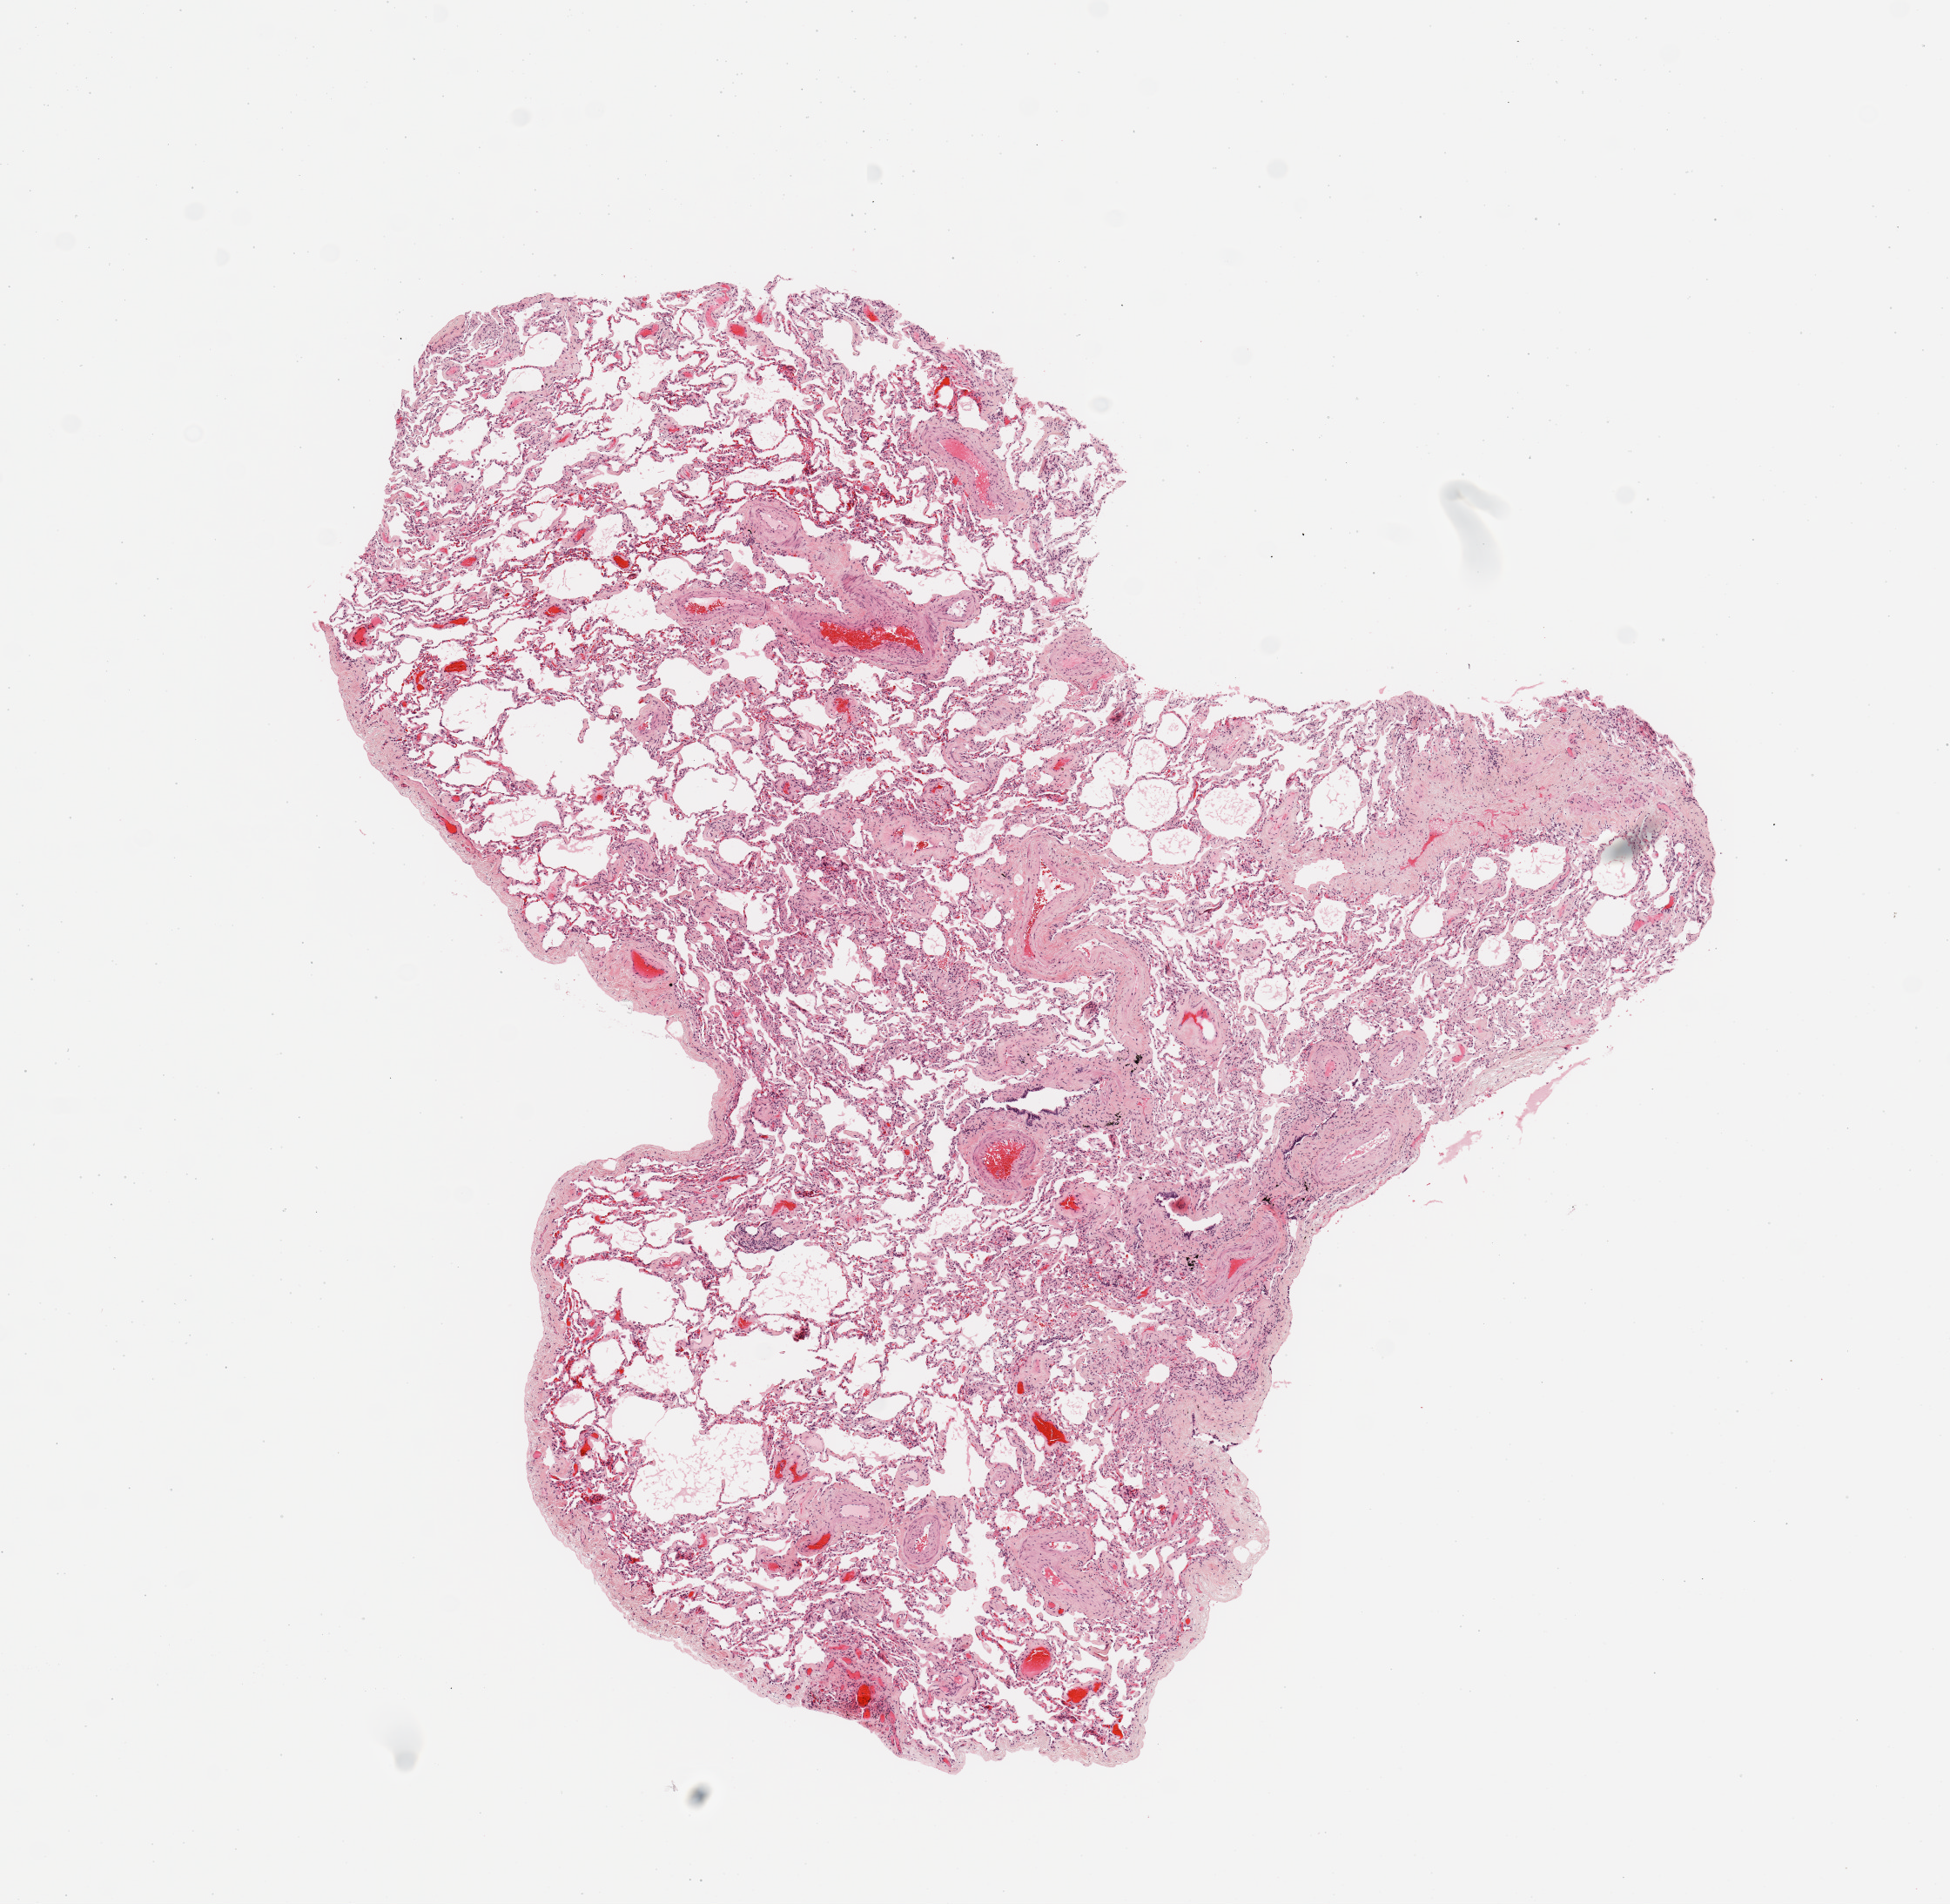
Whole-slide histology image, Hematoxylin and eosin (H&E) stained — low-resolution overview of the scanned area, about 8.9 x 8.6 mm (from a 20x scan). Normal (non-tumour) tissue sample, sampled site: lung. Male, 74 y/o.
* this section: normal (non-tumour) tissue from the same patient
* patient diagnosis: Adenocarcinoma, NOS